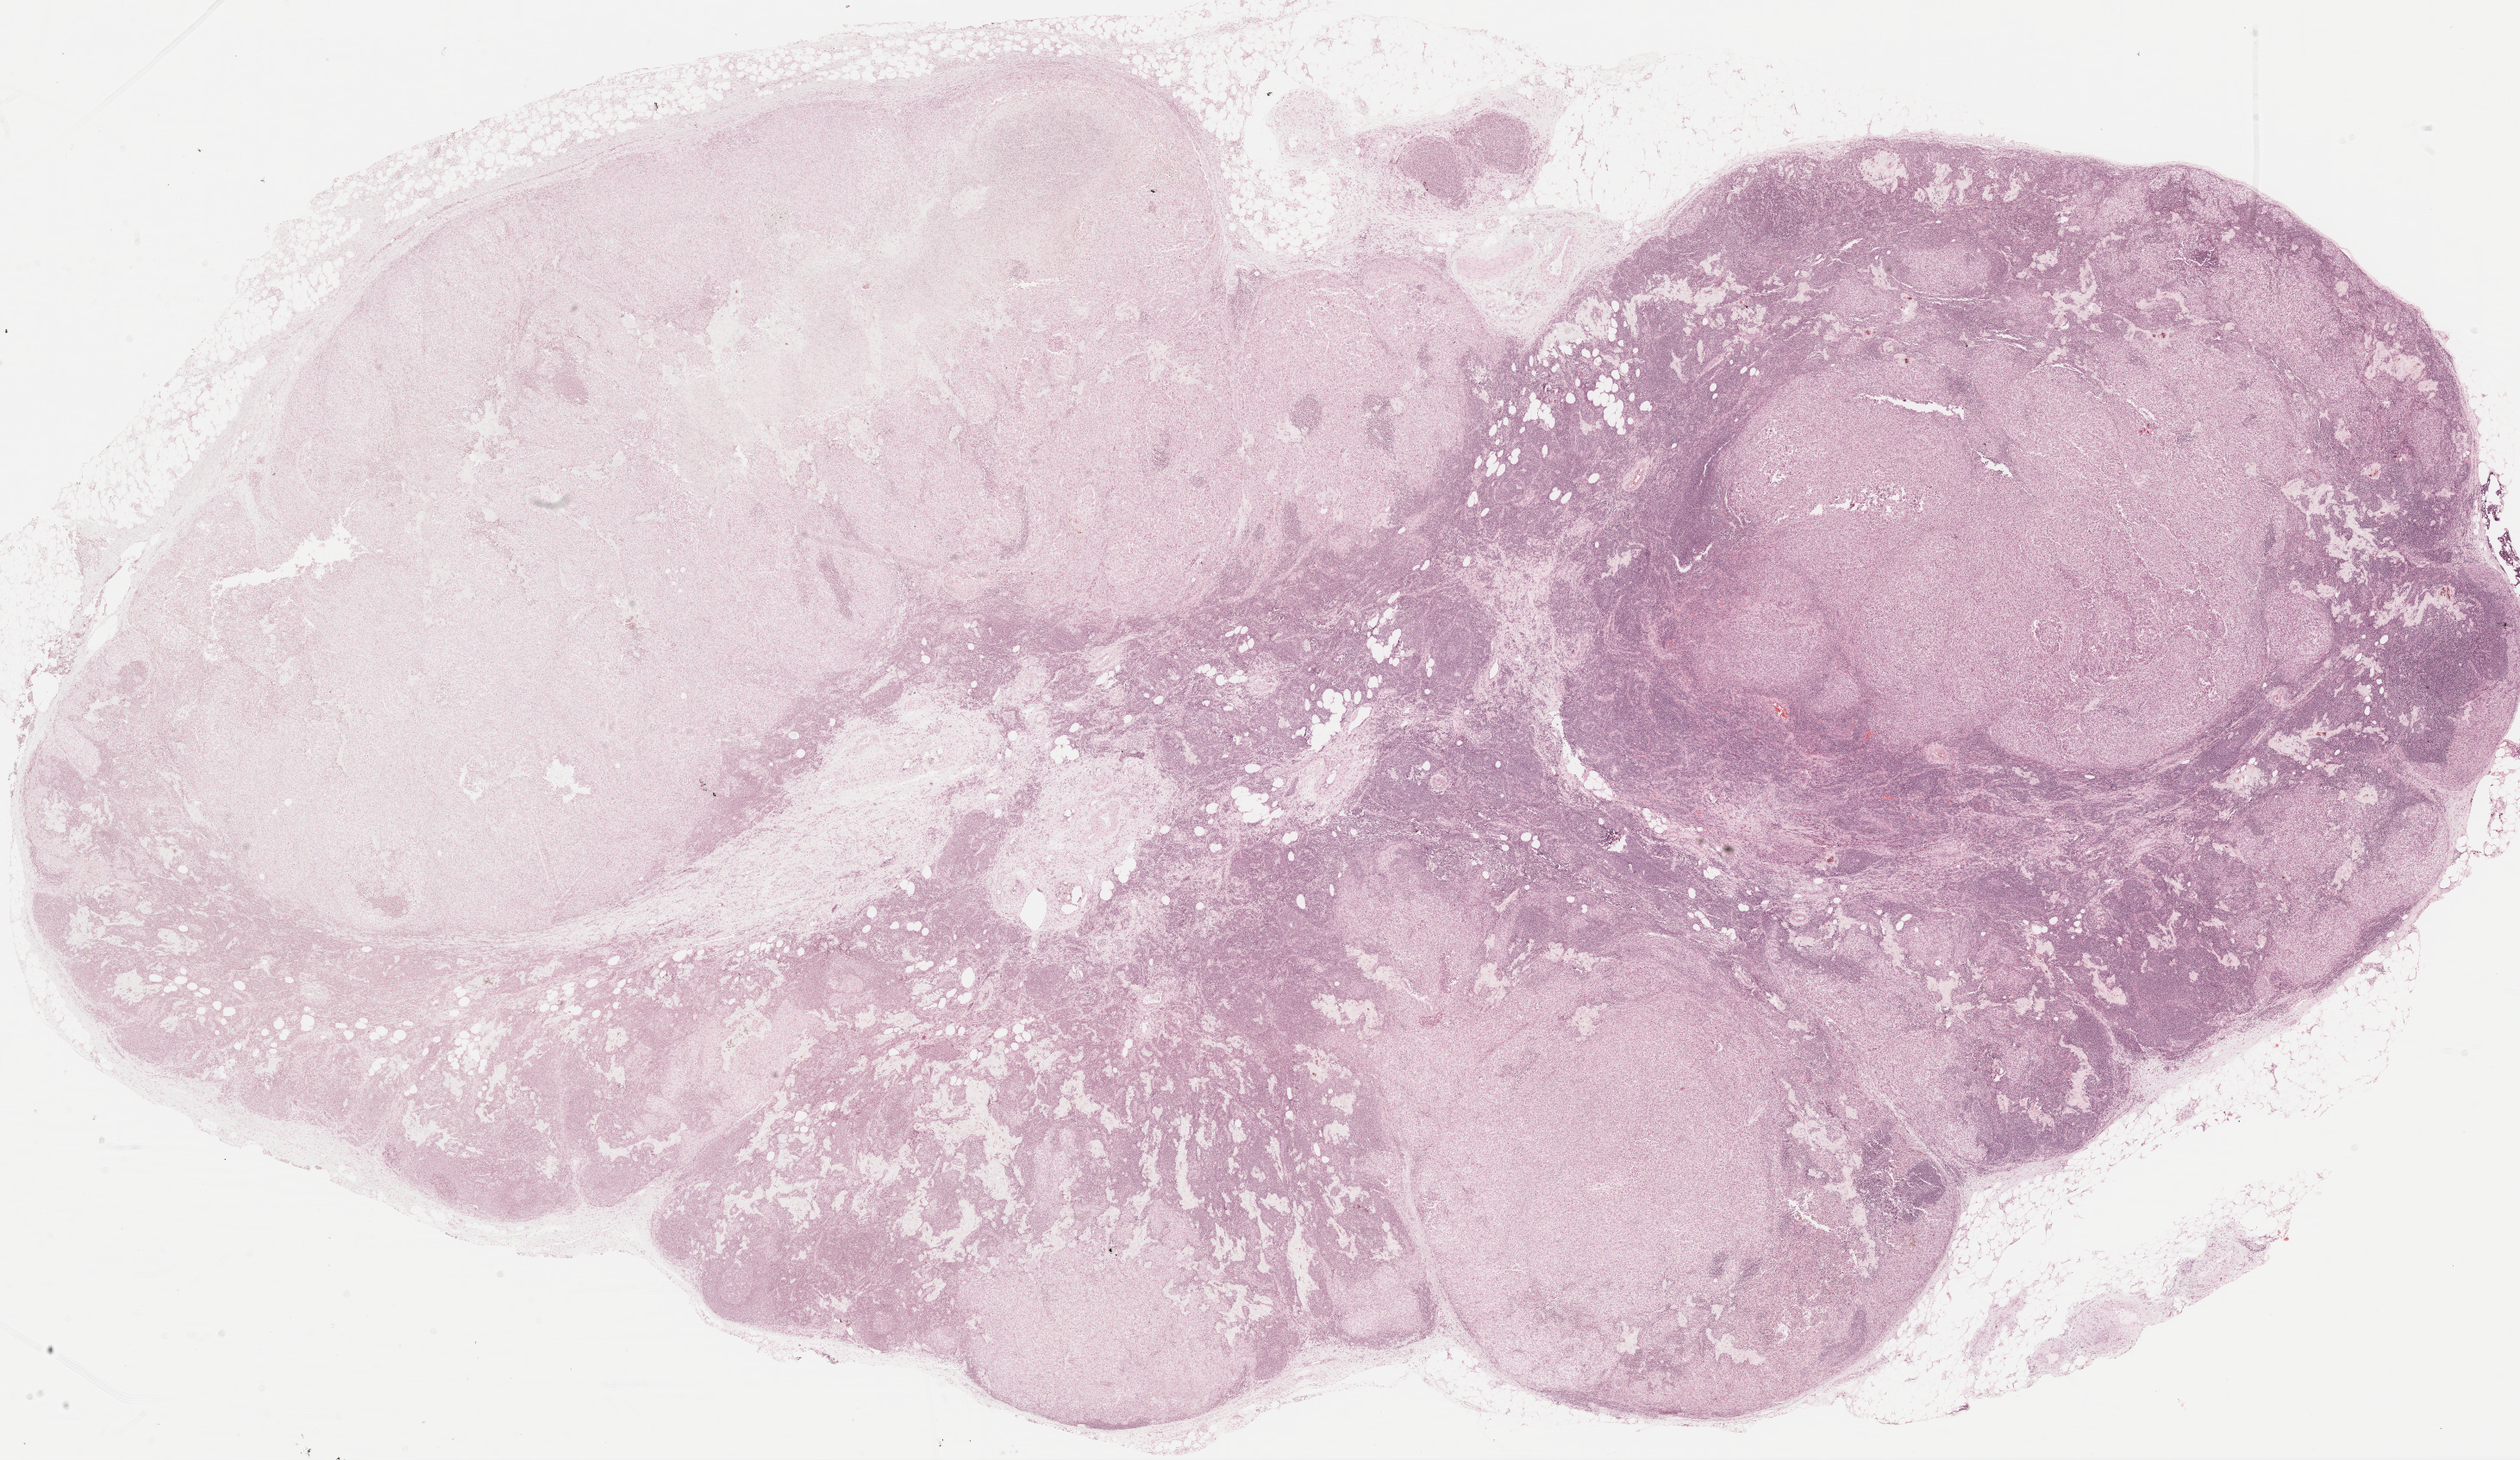
Digitized H&E-stained tissue section (whole slide), low-resolution overview of the scanned area, about 23.6 x 13.7 mm; FFPE section; metastatic tumour sample, sampled site not recorded. Patient: female, age at initial diagnosis 61 years.
- this section: metastatic tumour tissue
- patient diagnosis: Malignant melanoma, NOS